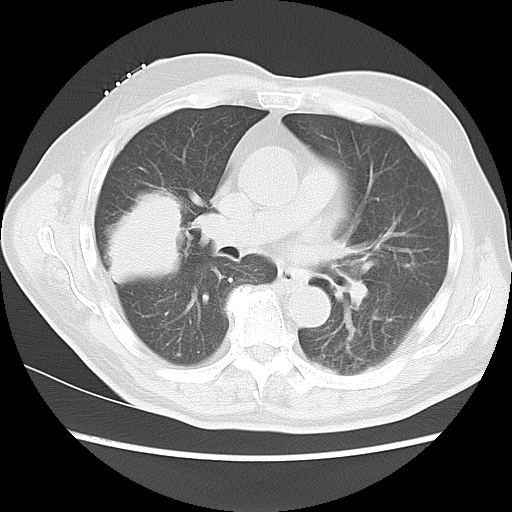
Chest CT, one axial slice. Position 5 of 15 along the scan axis. Reconstruction kernel LUNG. 120 kVp. Lung window (W 1500 / L -600 HU). 5 mm slice thickness. 512 × 512 image matrix. Male patient, age 68 years. Case-level facts recorded for this patient, not image findings: clinical TNM (as recorded): T4 N3 M0.
Structures marked on this image (rectangle marked by the reading radiologist):
- lung tumour (recorded histology: squamous cell carcinoma): bounding box [x1, y1, x2, y2] px = [95, 177, 190, 290]